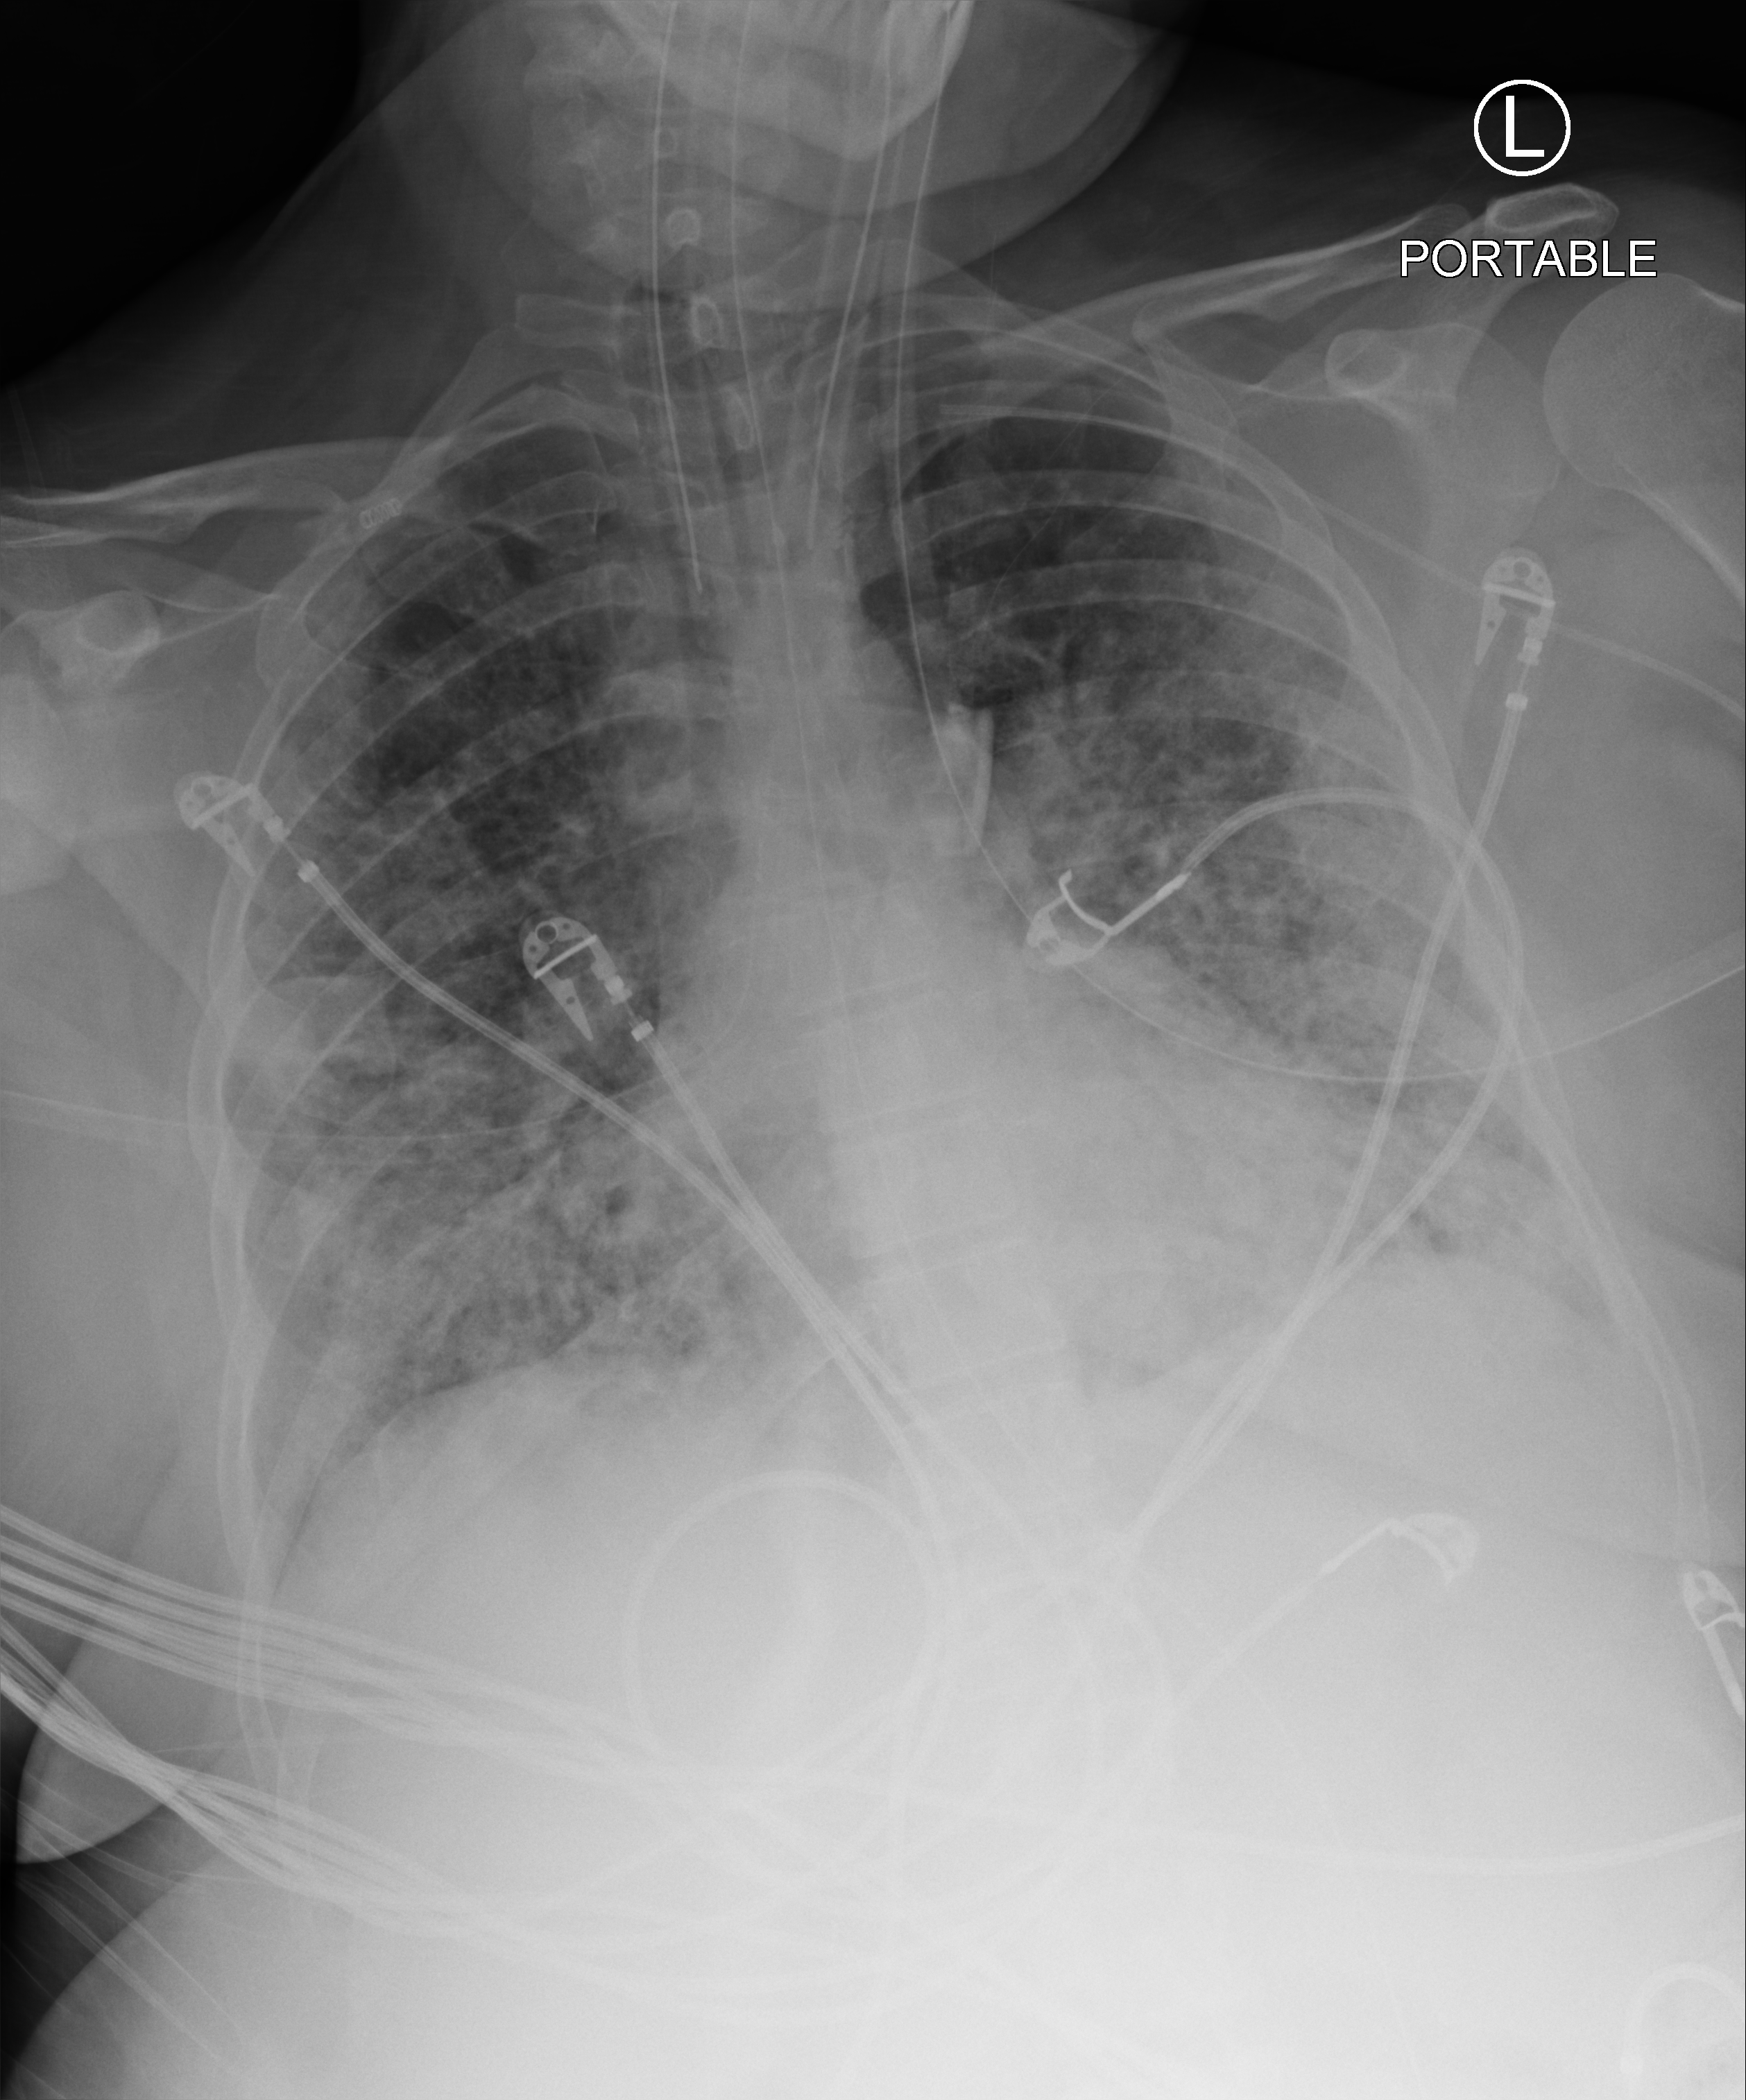
Chest X-ray (portable). Patient hospitalised with COVID-19; female, aged 18–59 years.
Admission-level facts for this patient (not findings on this image; timing relative to this image not recorded): admitted to intensive care during this hospital stay: yes; COPD (admission record): no; mechanically ventilated during this hospital stay: yes.